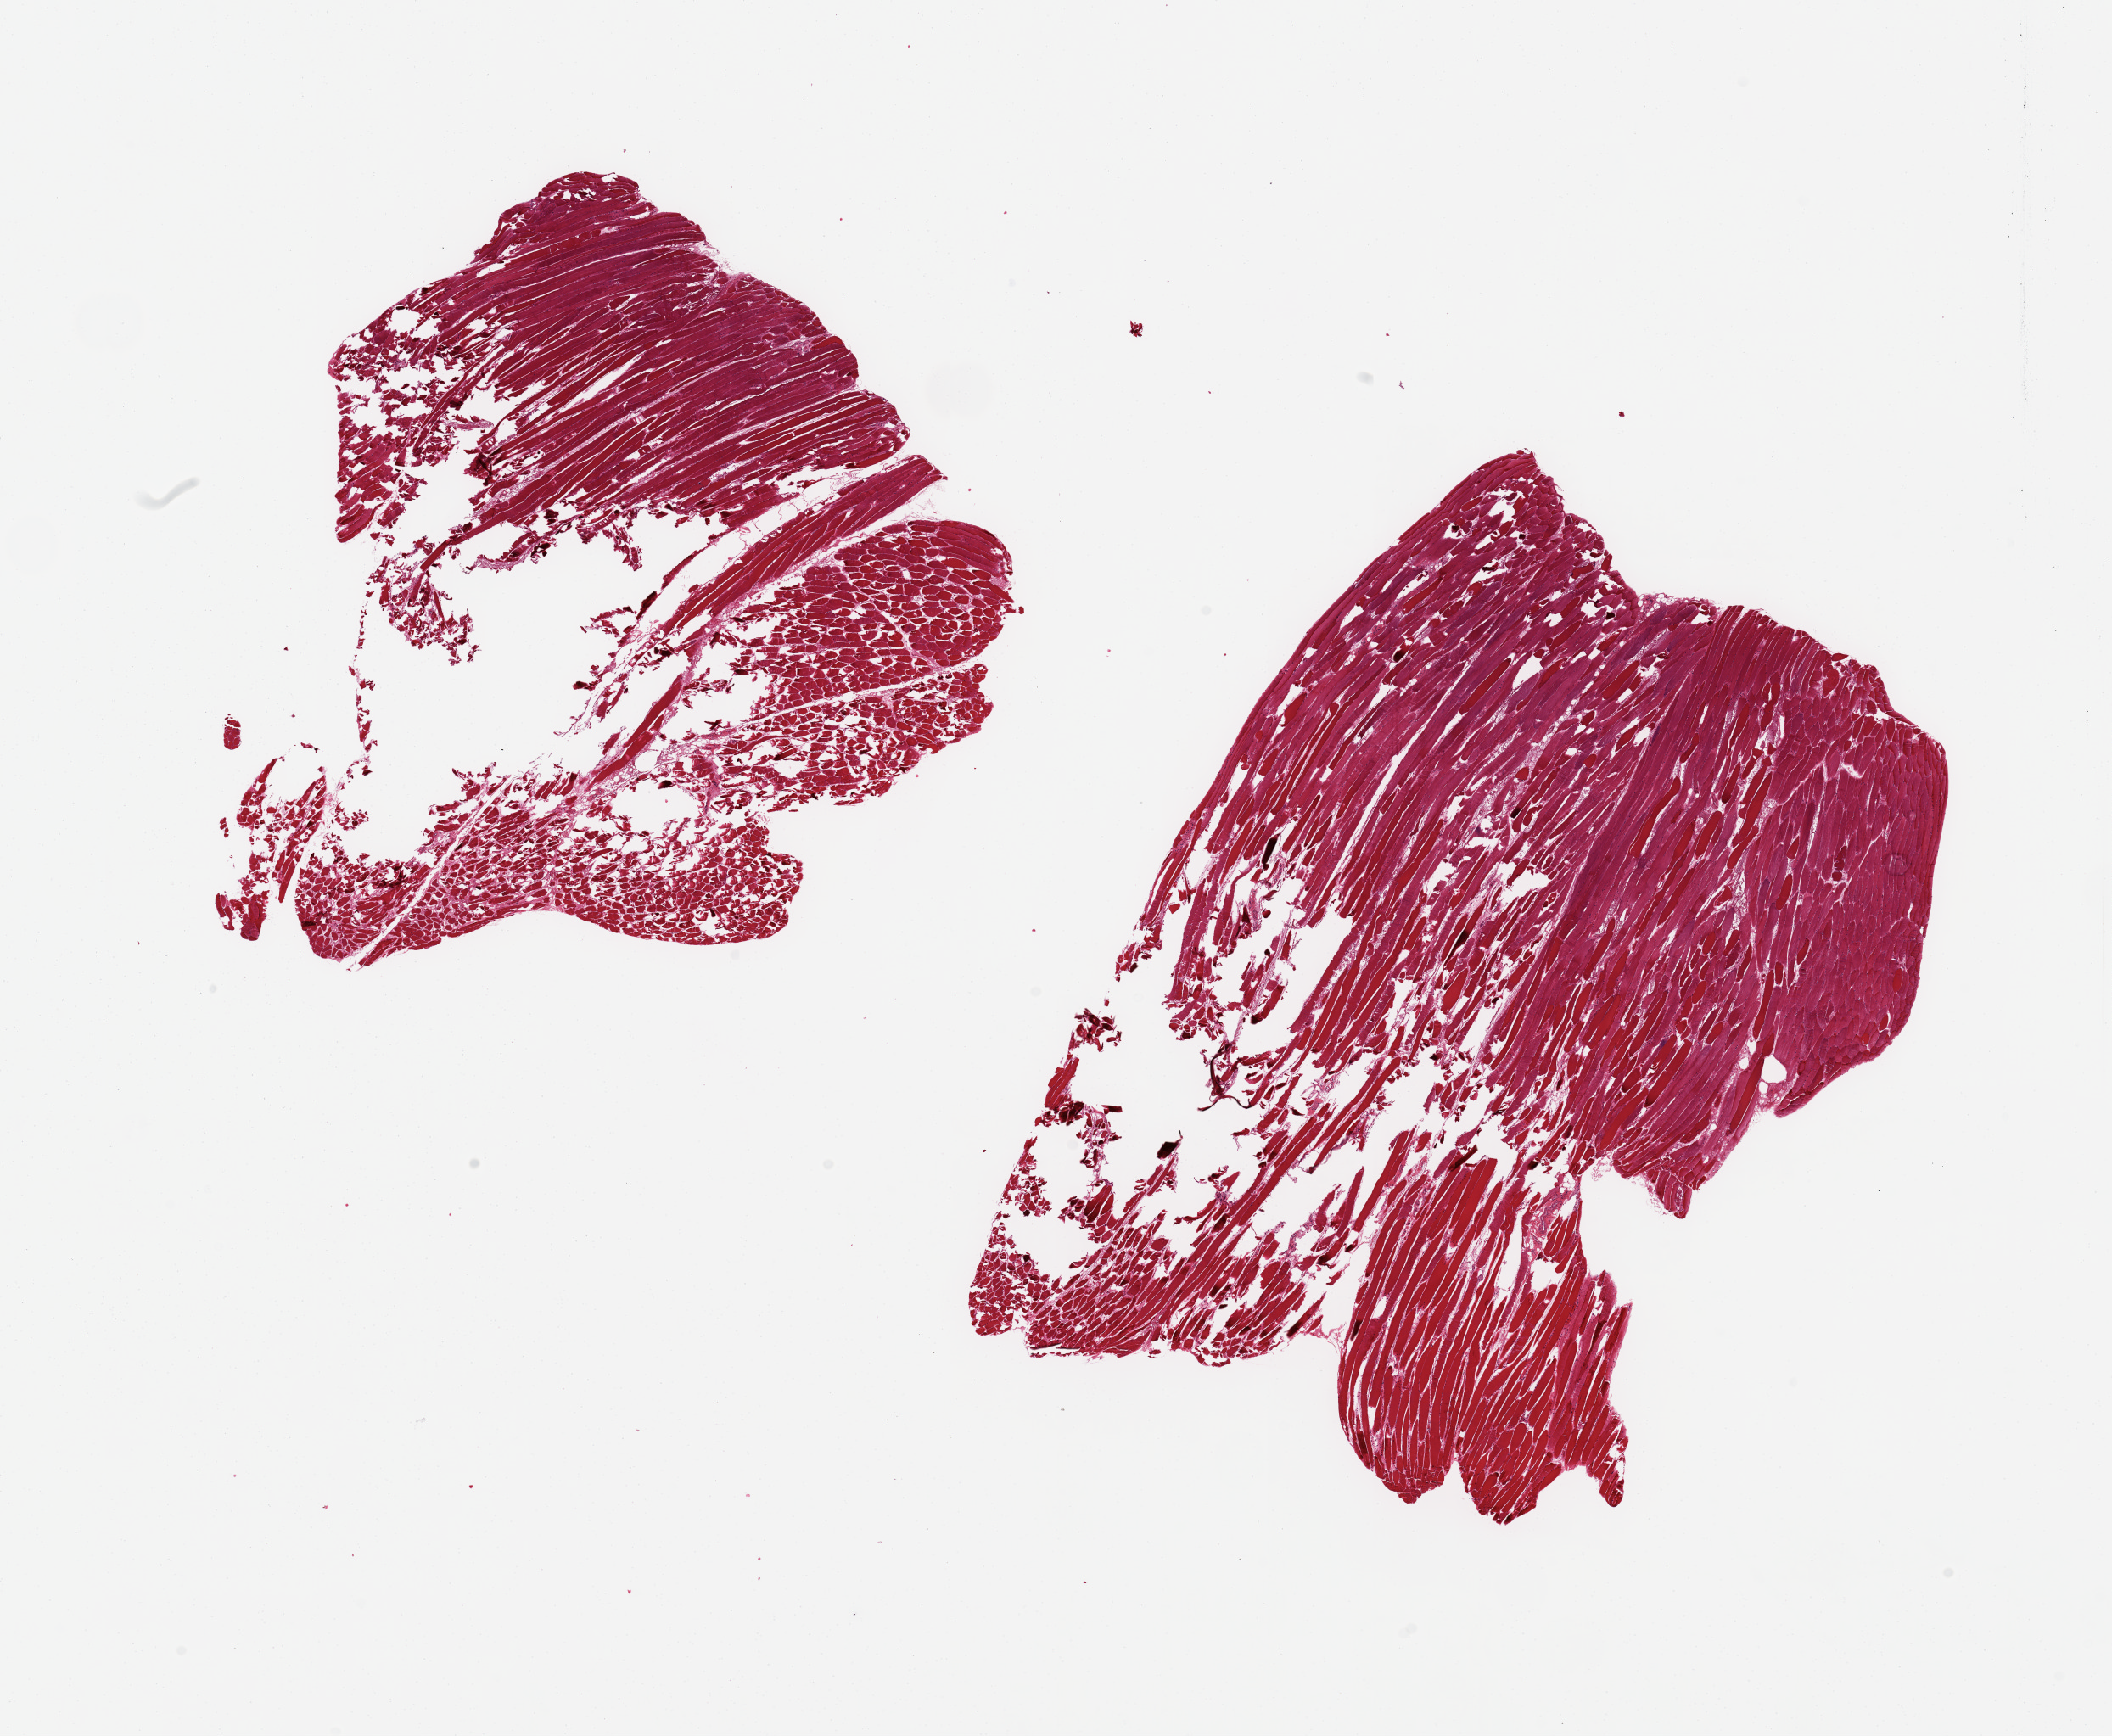
Digitized haematoxylin and eosin-stained section — a low-resolution overview of the entire scanned area, about 19.7 x 16.2 mm (acquisition: 20x scan). PAXgene-fixed, paraffin-embedded tissue. Section of skeletal muscle (target tissue). Tissue donor sample. Donor: male.
* reviewer comment on this tissue sample: 2 pieces 7x6 & 9x7 mm; severe fracture artifacts appear histologic not fixation